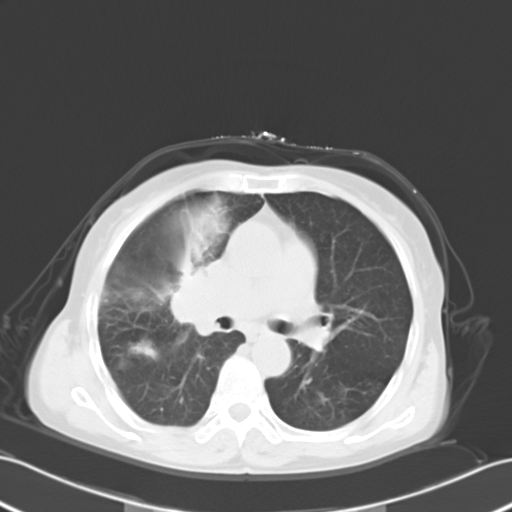
Chest CT, one axial slice. Slice 16 of 27 in the series (ordered by position). Lung window (W 1500 / L -600 HU). 10 mm slice thickness. 512 × 512 image matrix, field of view 353 × 353 mm. Patient: female, 67 years. From the clinical record (not read from this slice): clinical TNM (as recorded): T2a N3 M0; histopathological grade: G3.
Structures marked on this image (bounding box drawn by a radiologist):
- lung tumour (recorded histology: small cell carcinoma): bounding box <167,254,231,342> (left, top, right, bottom; pixels)